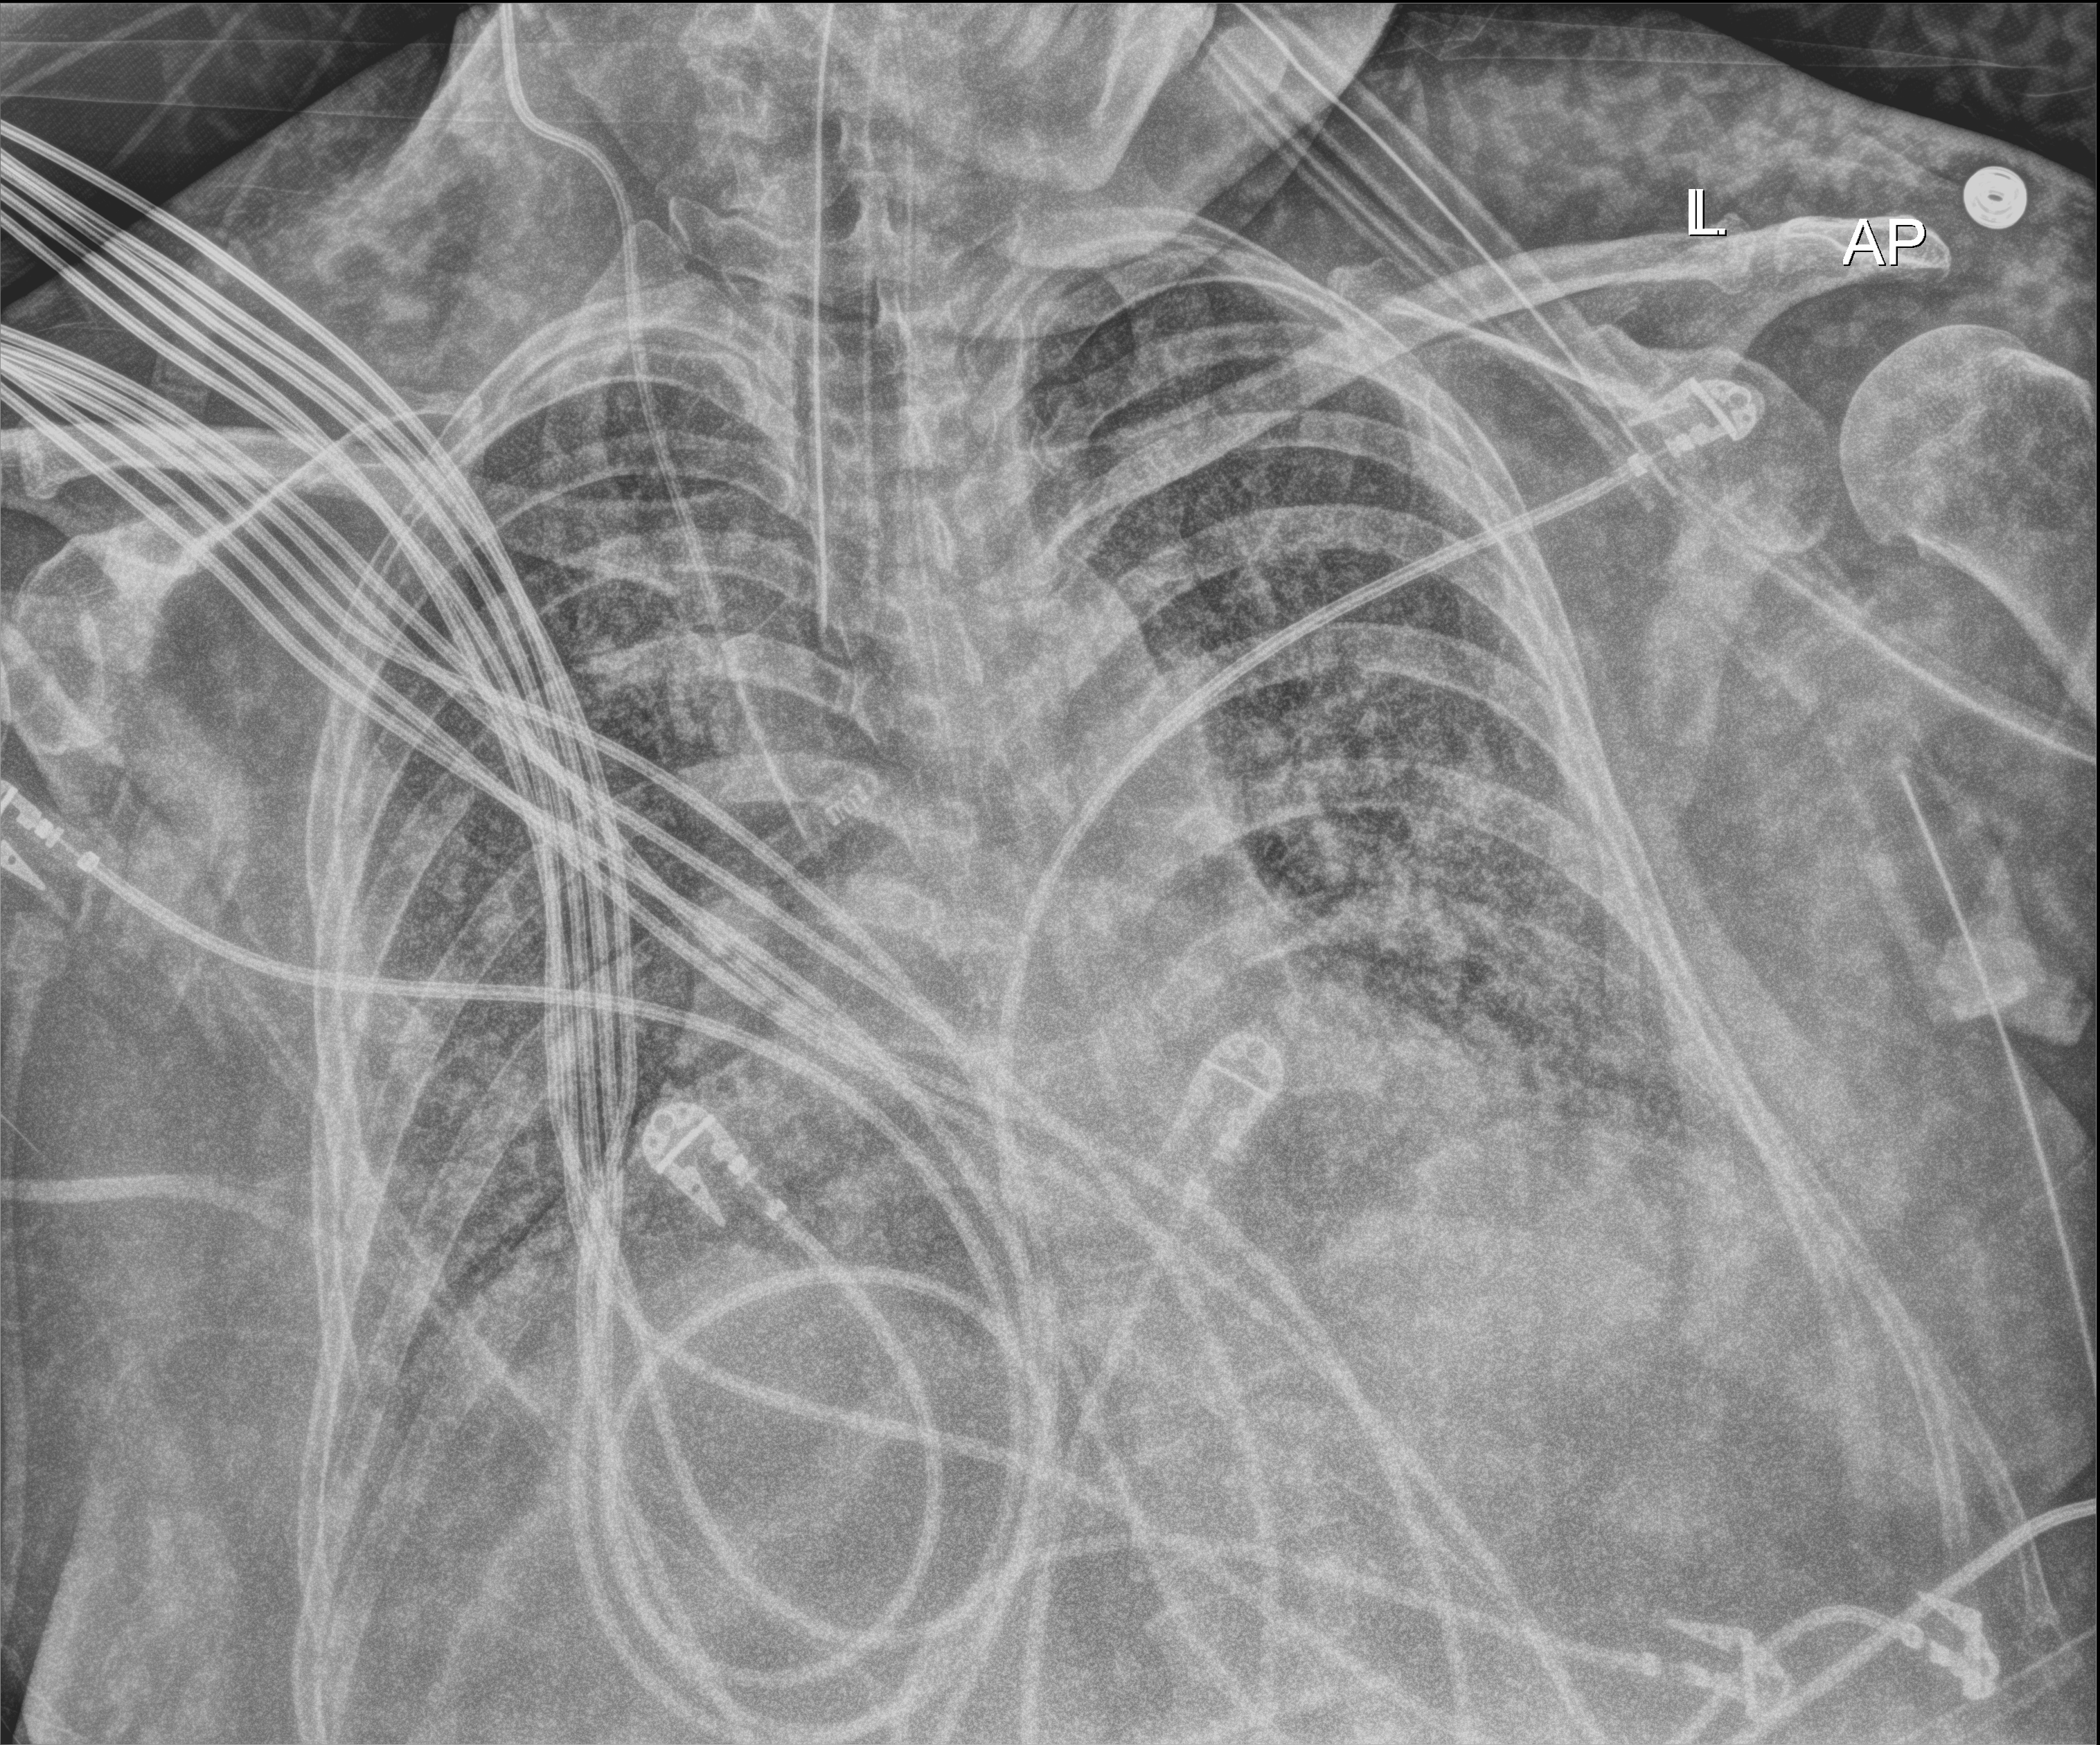
Bedside chest radiograph (digital radiography); anteroposterior (AP) projection. Adult patient hospitalised with COVID-19, age 18–59 years.
From the hospital-stay record, not from the radiograph (when in the stay this image was taken is not recorded):
- mechanically ventilated during this hospital stay: yes
- admitted to intensive care during this hospital stay: yes